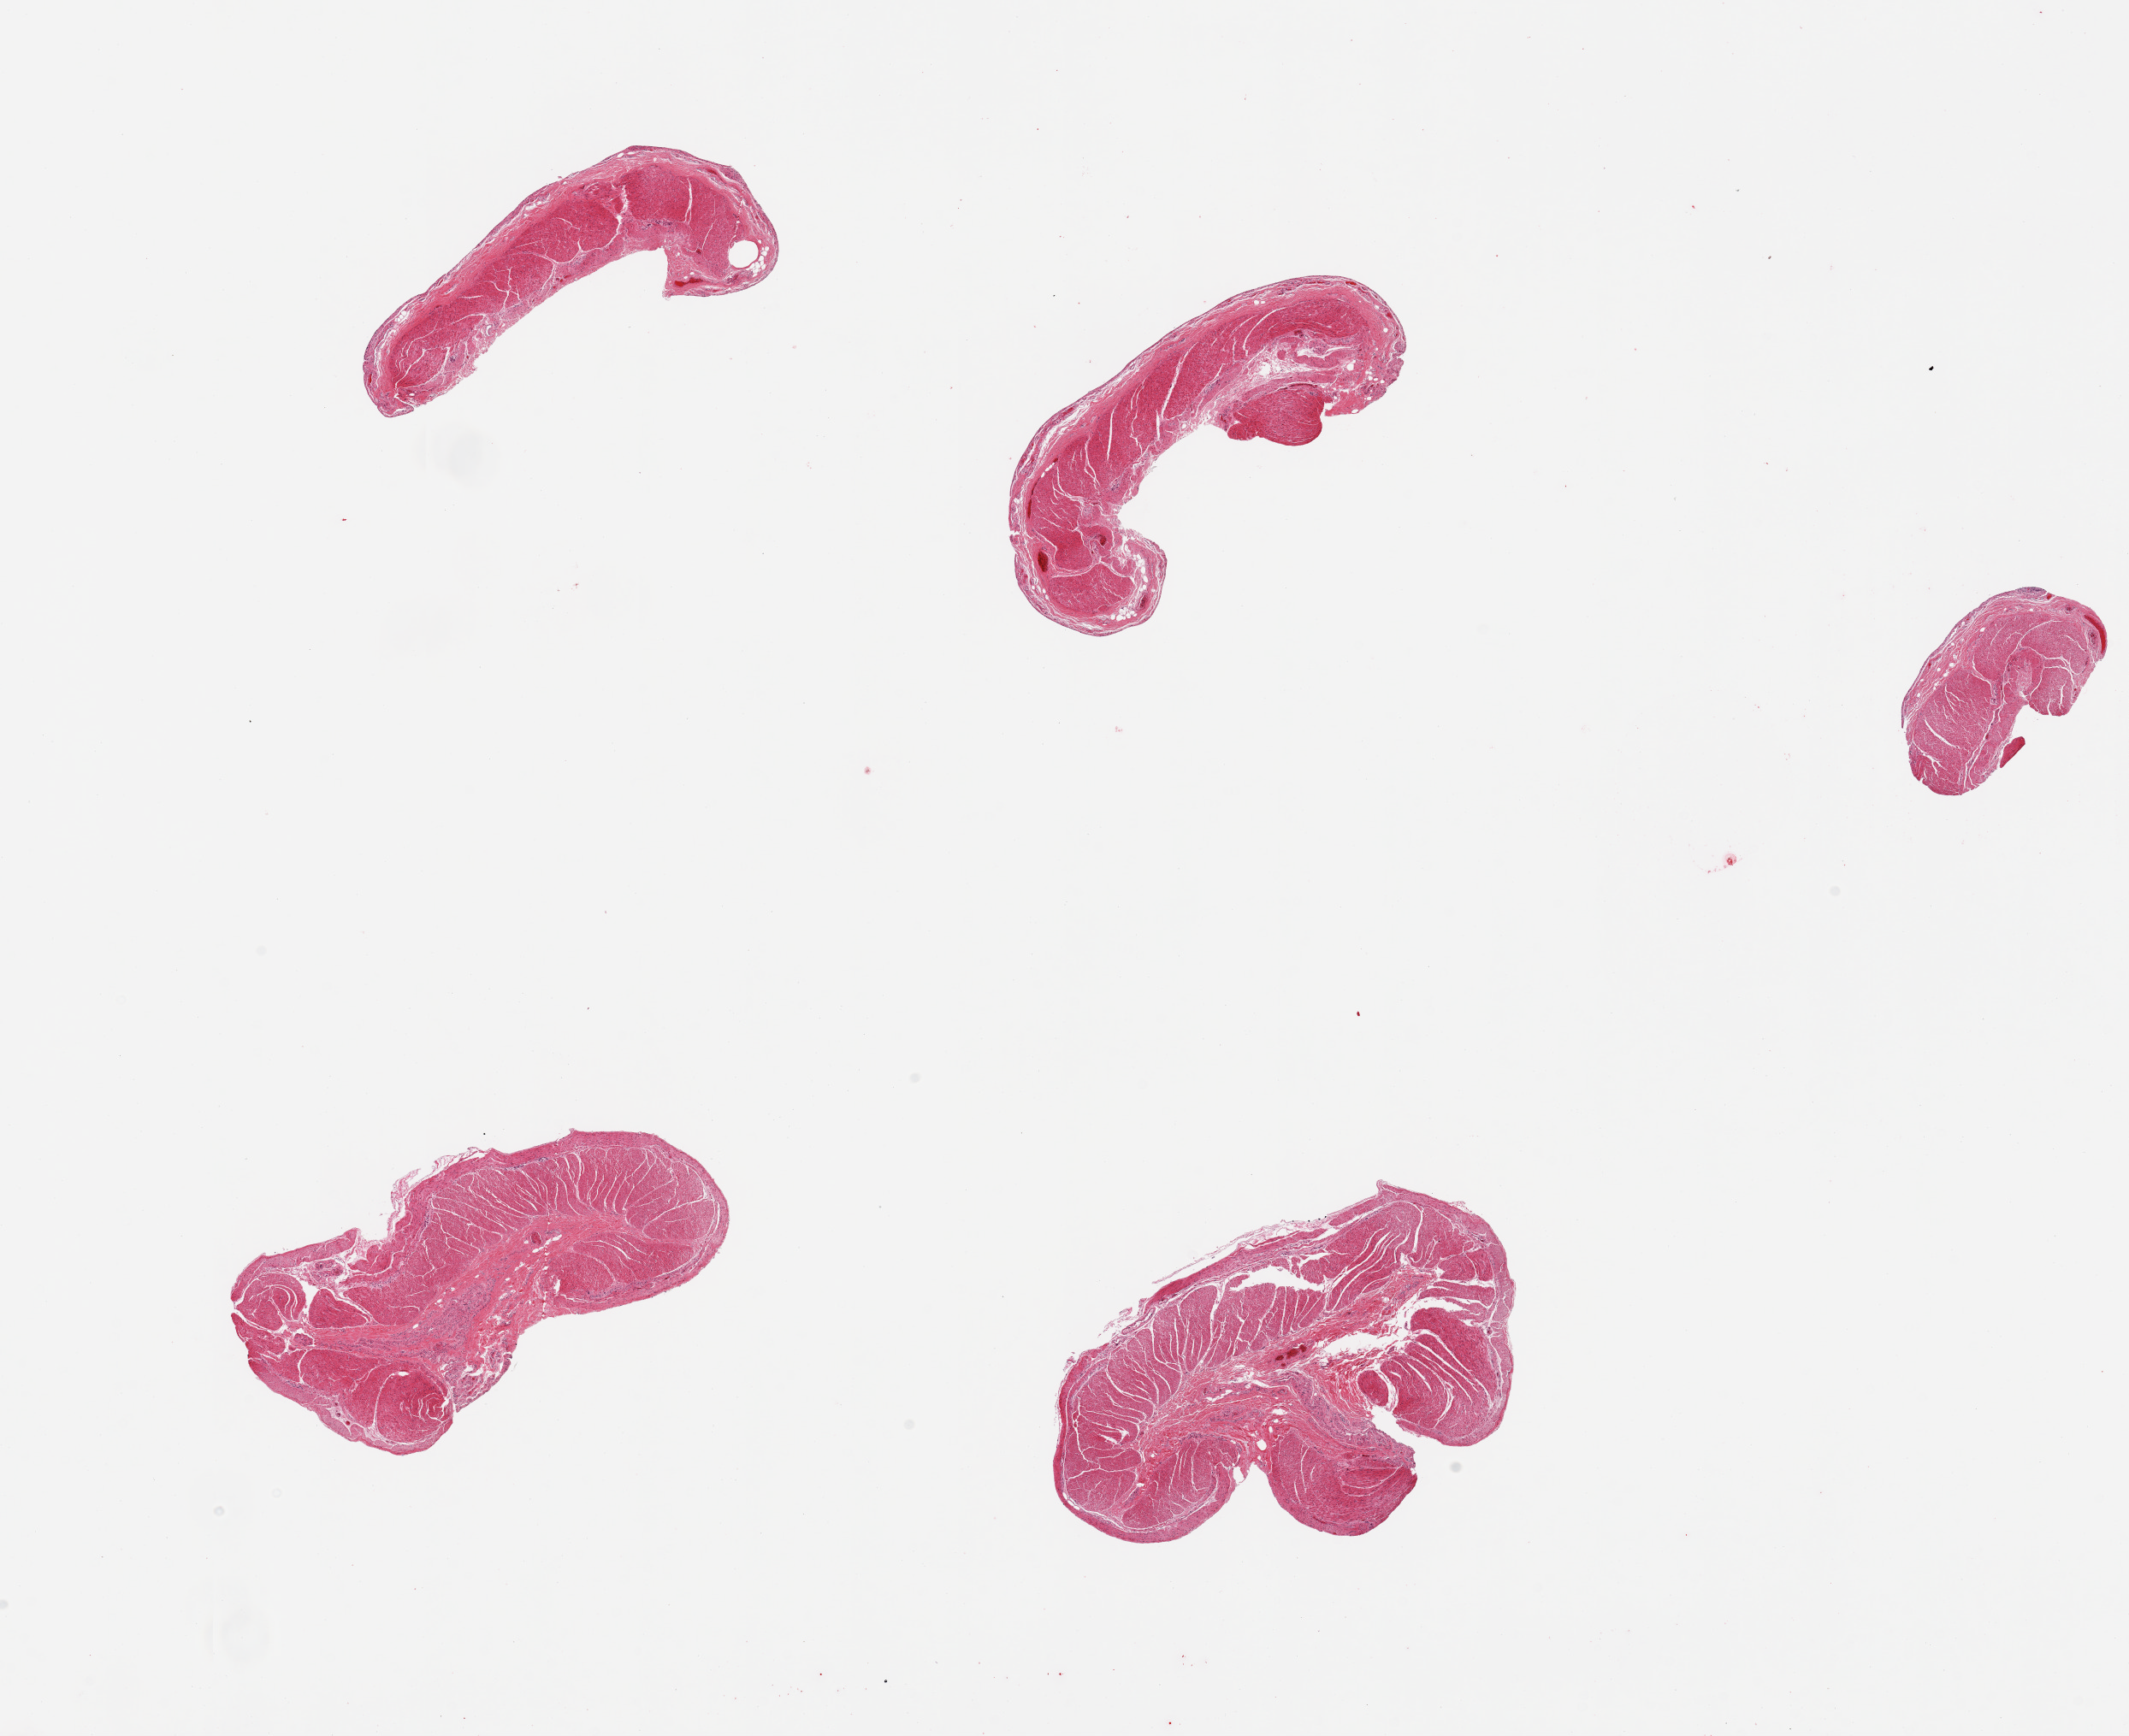
Whole-slide image, hematoxylin and eosin (H&E) stain, brightfield, low-resolution overview of the scanned area, about 19.7 x 16.1 mm (slide scanned at 20x); PAXgene-fixed, paraffin-embedded tissue; target tissue: sigmoid colon; tissue donor sample. Female donor.
Pathologist's review note for this sample: 6 pieces; well trimmed.